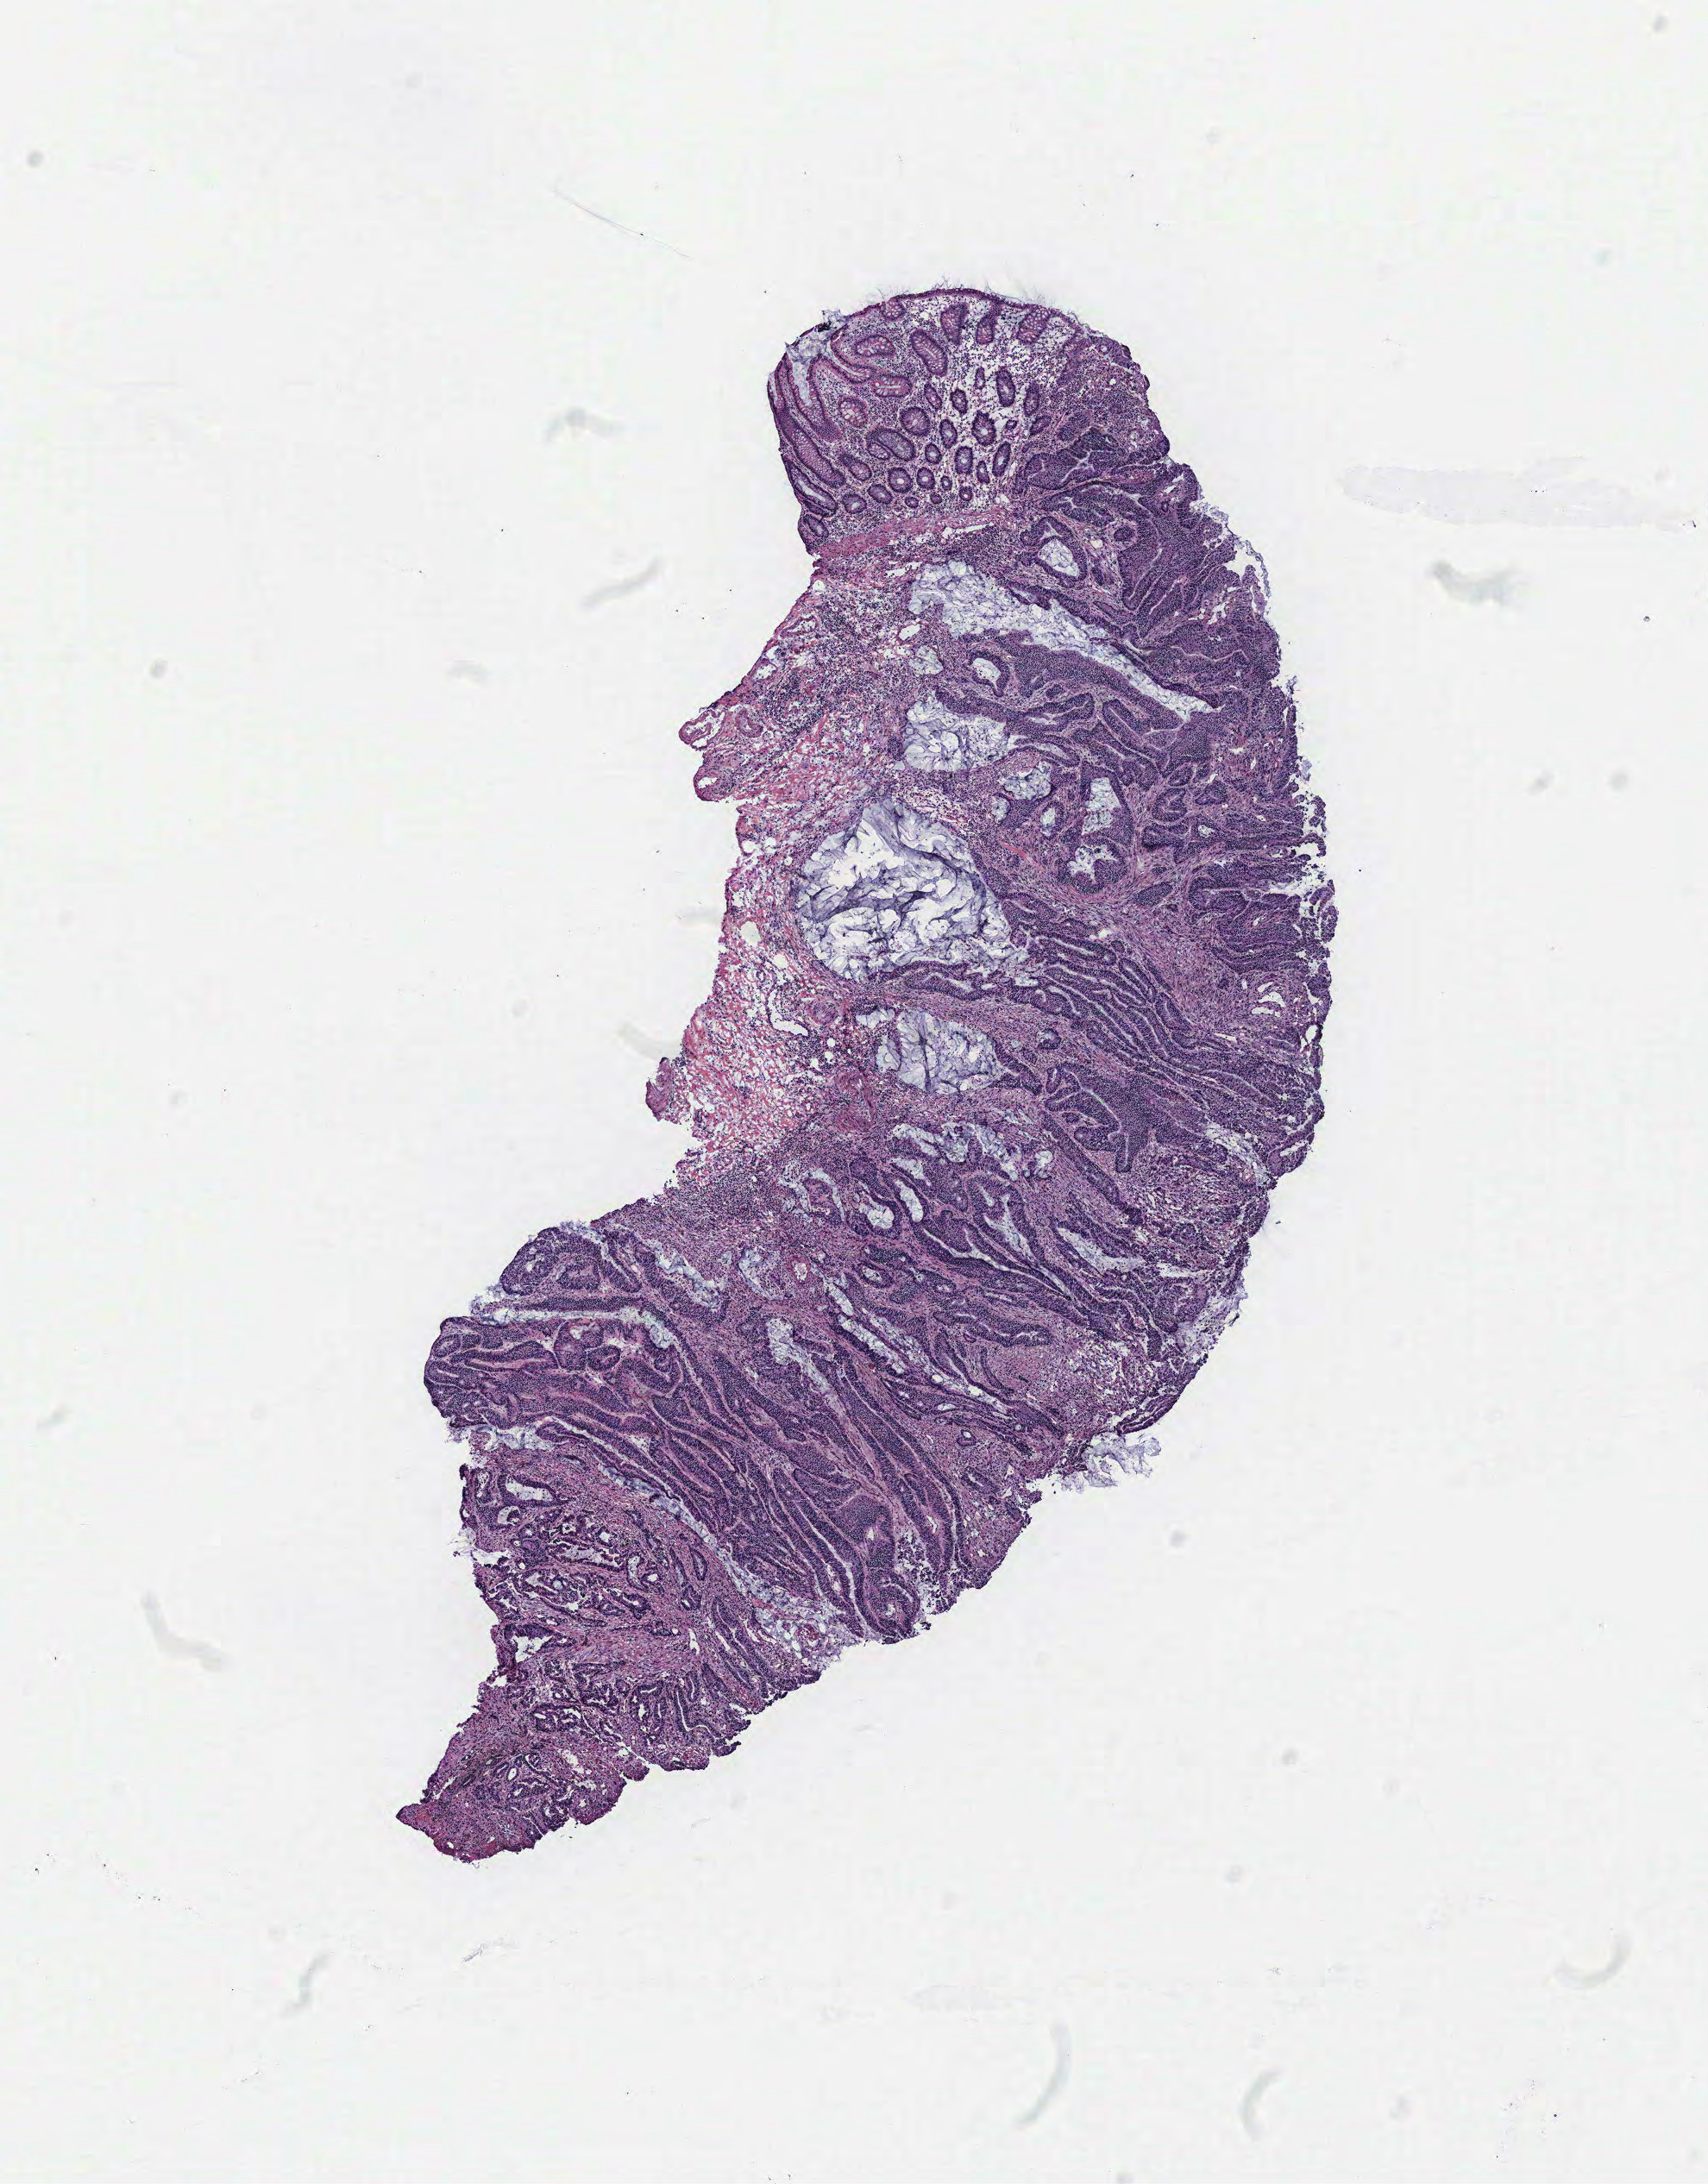
Digitized H&E tissue section (whole slide), low-resolution overview of the scanned area, about 7.9 x 10.1 mm, normal (non-tumour) tissue sample, colon. Patient: male, age 79 years.
• this section: normal (non-tumour) tissue from the same patient
• patient diagnosis: Adenocarcinoma, NOS